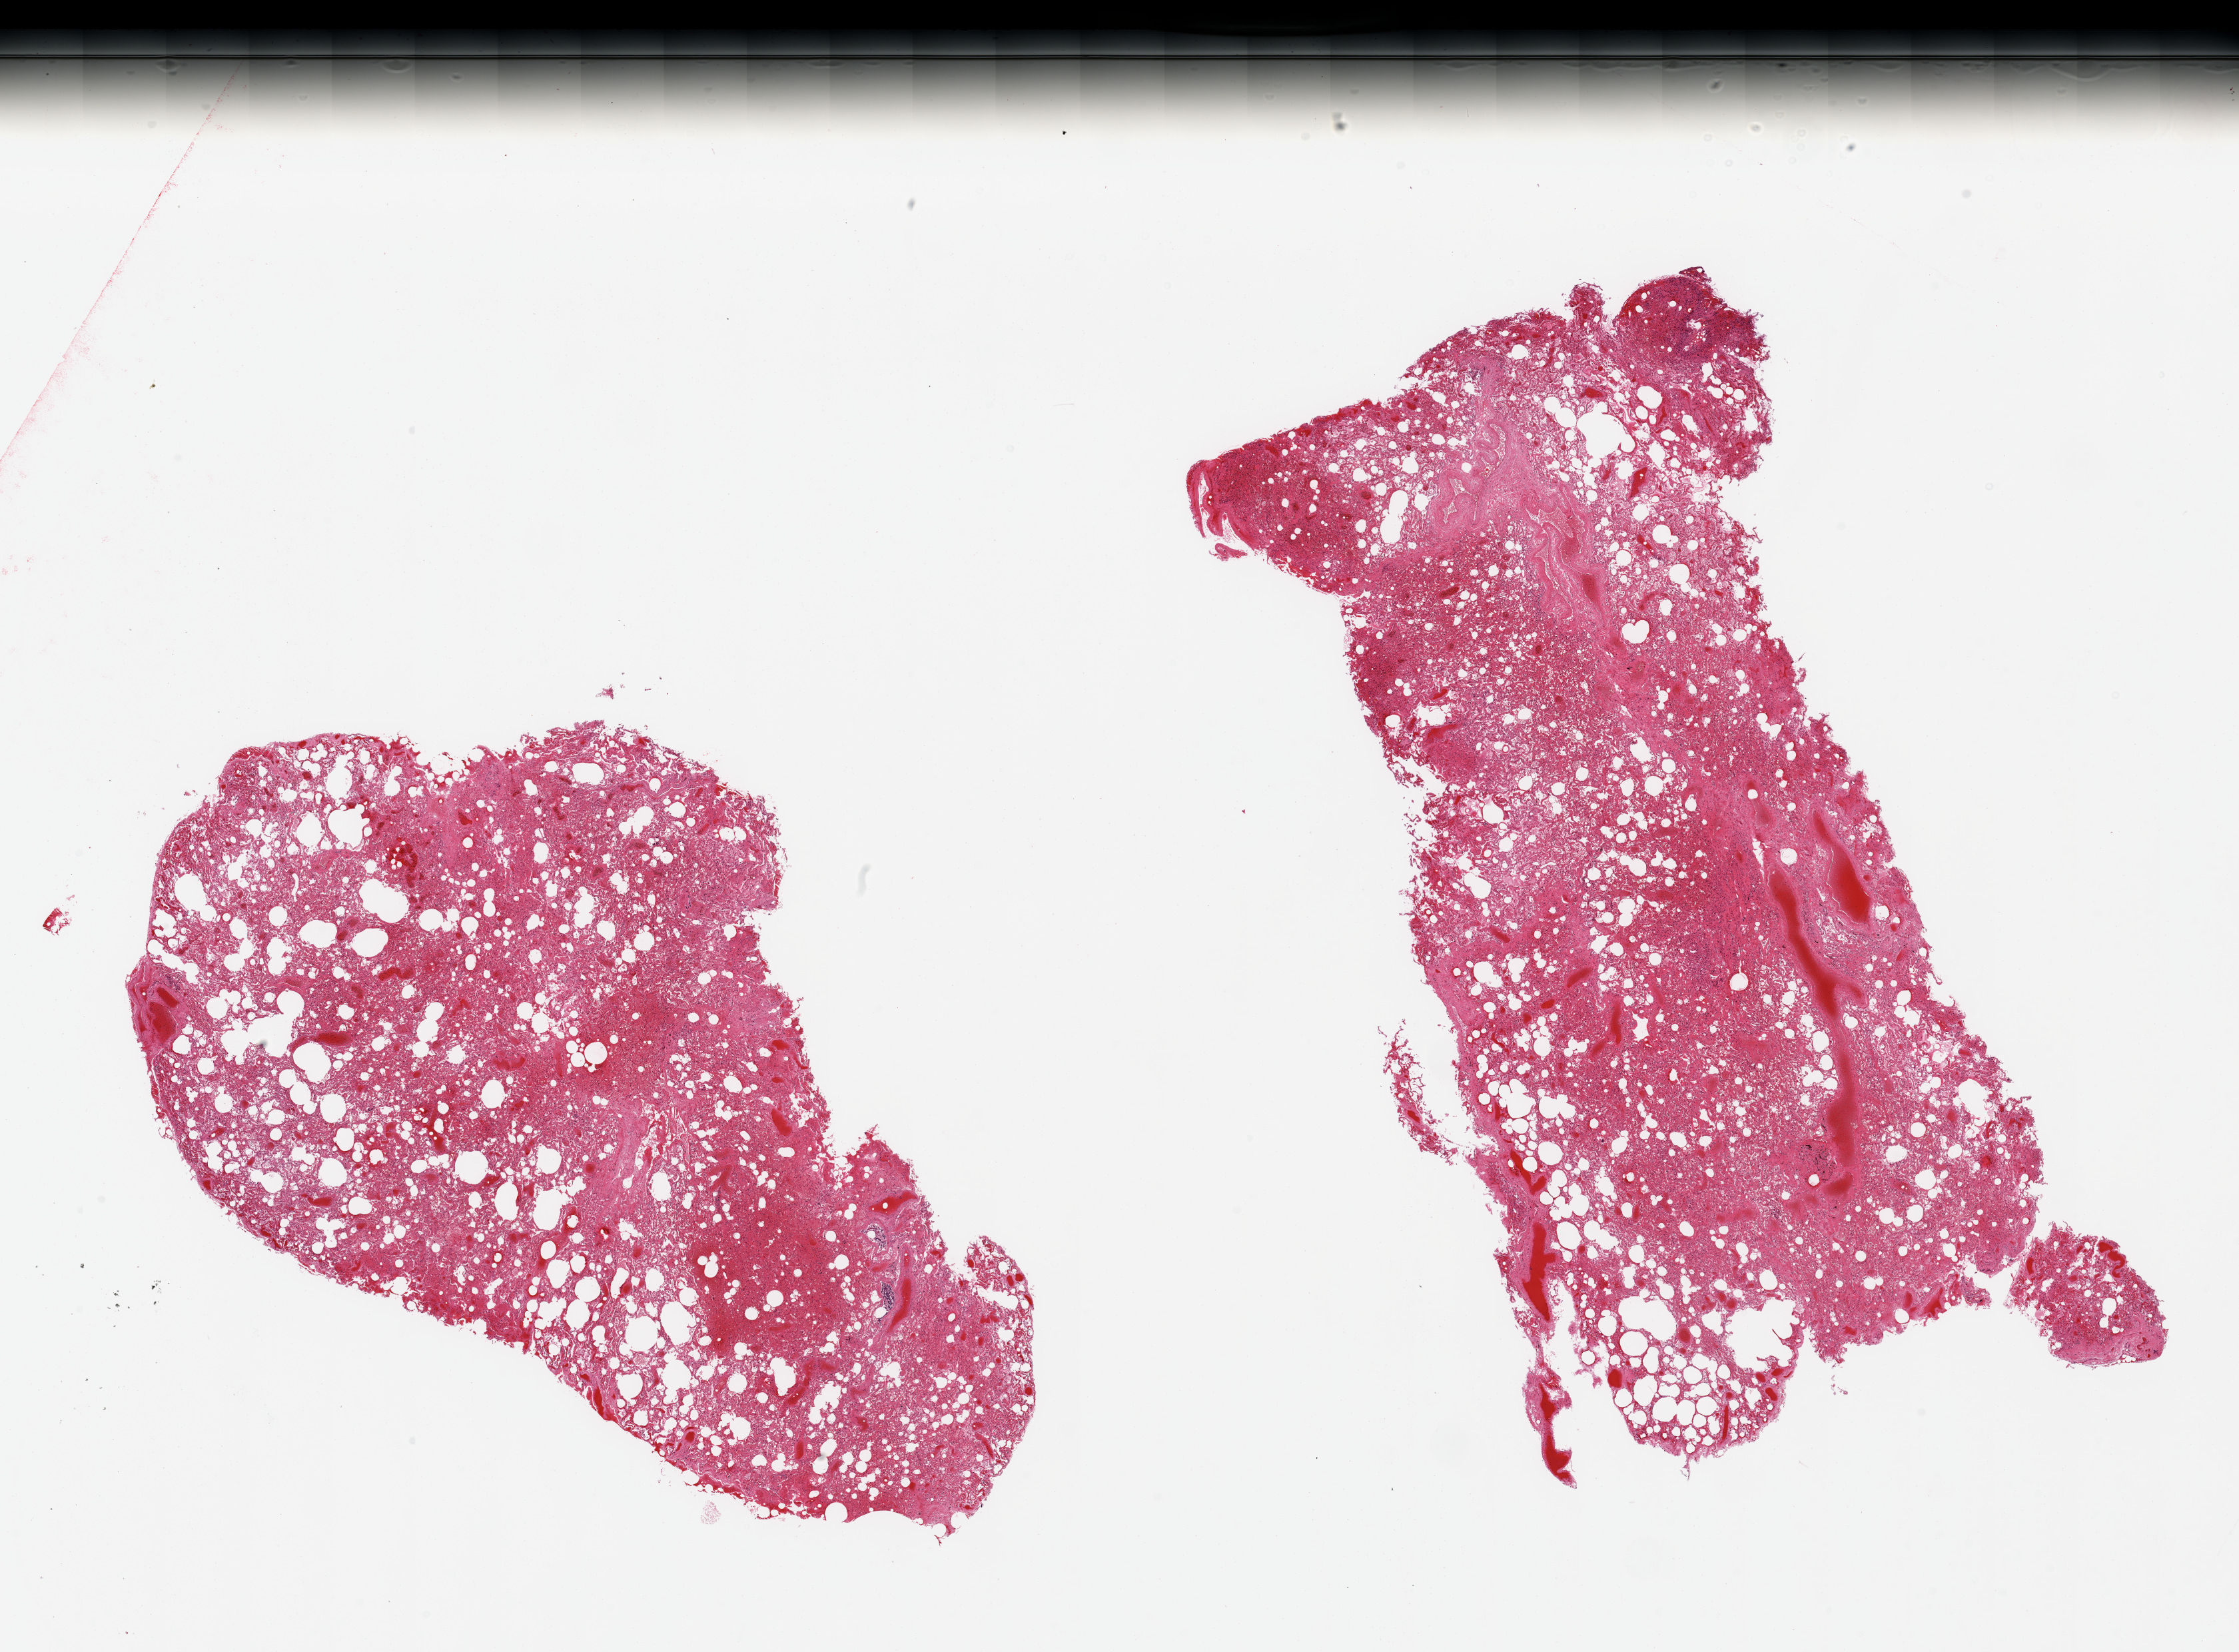
Whole-slide image, H&E stain, brightfield — whole scanned area (about 26.6 x 19.6 mm, acquisition: 20x scan) shown as a low-resolution overview; PAXgene-fixed, paraffin-embedded tissue; section of lung (target tissue); donor tissue sample. Donor sex: male.
* reviewer comment on this tissue sample: 2 pieces, congestion, edema, moderate/marked atalectasis